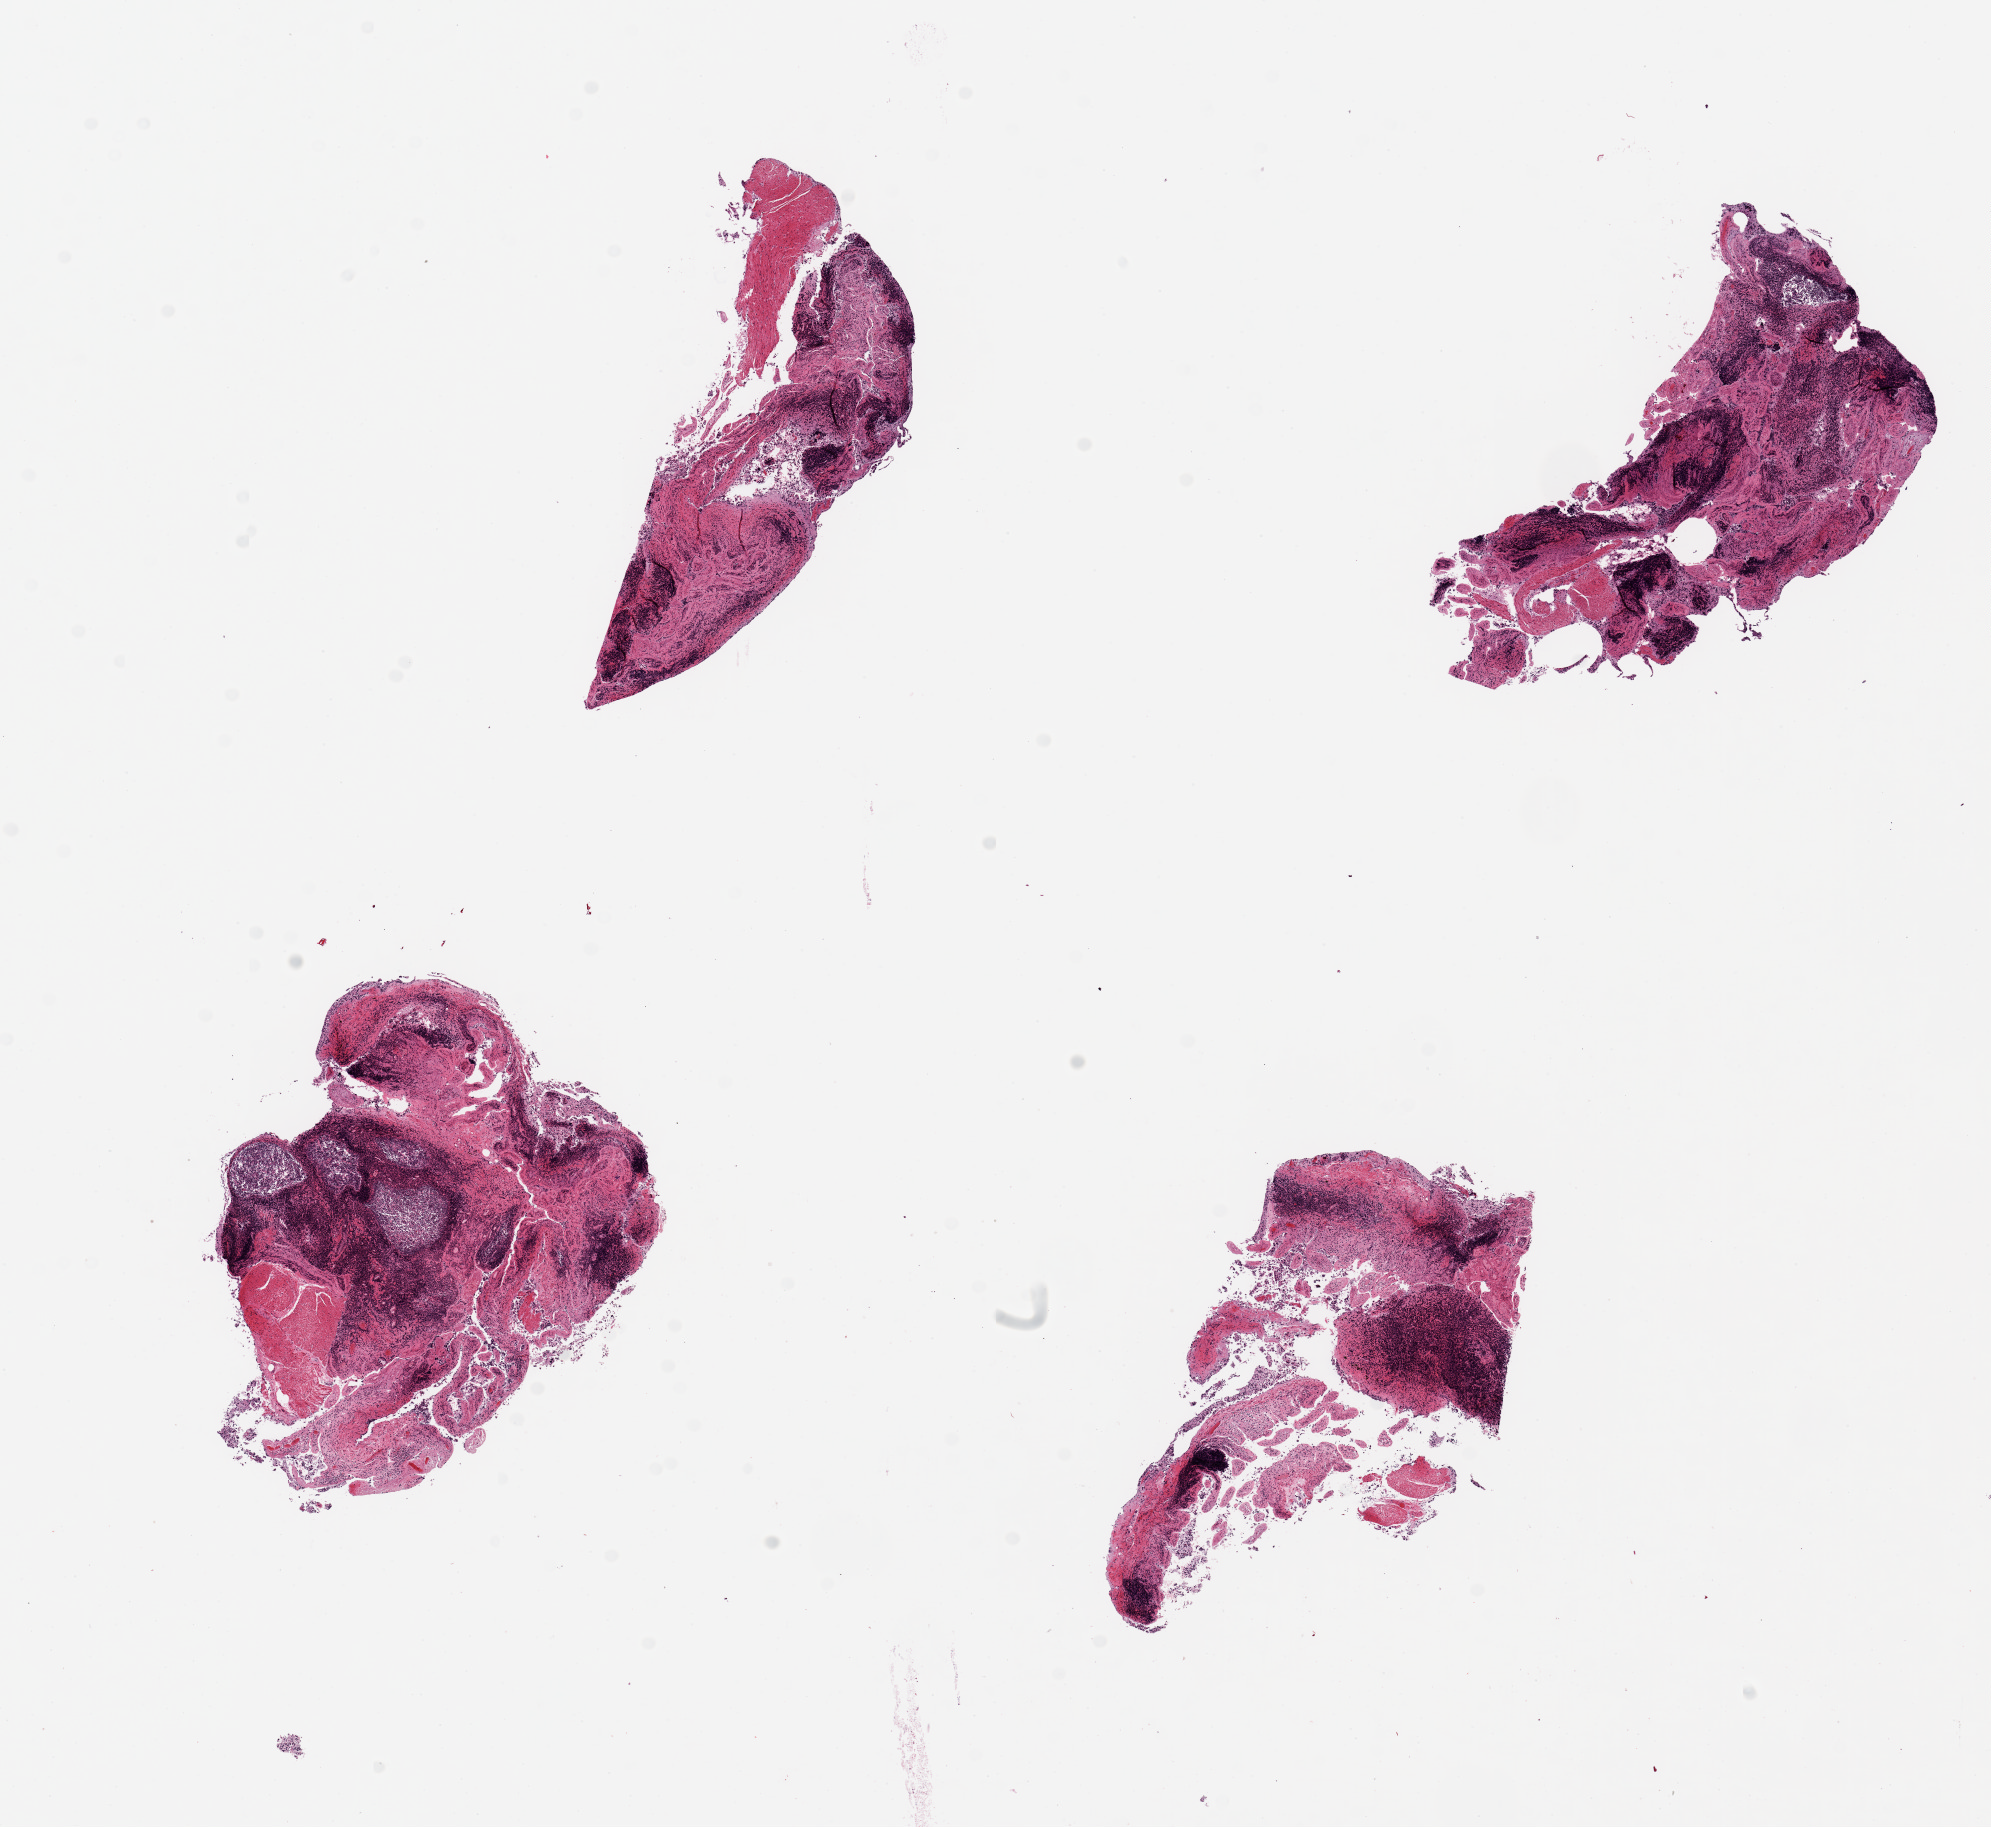
Haematoxylin and eosin whole-slide image, whole scanned area (about 15.8 x 14.5 mm) shown as a low-resolution overview; PAXgene-fixed, paraffin-embedded tissue; target tissue: ileum; tissue donor sample. Donor: male.
Reviewer comment on this tissue sample: 4 pieces ~4x2mm ~30% lymphoid elements but badly autolyzed mucosa. Minimal muscularis.